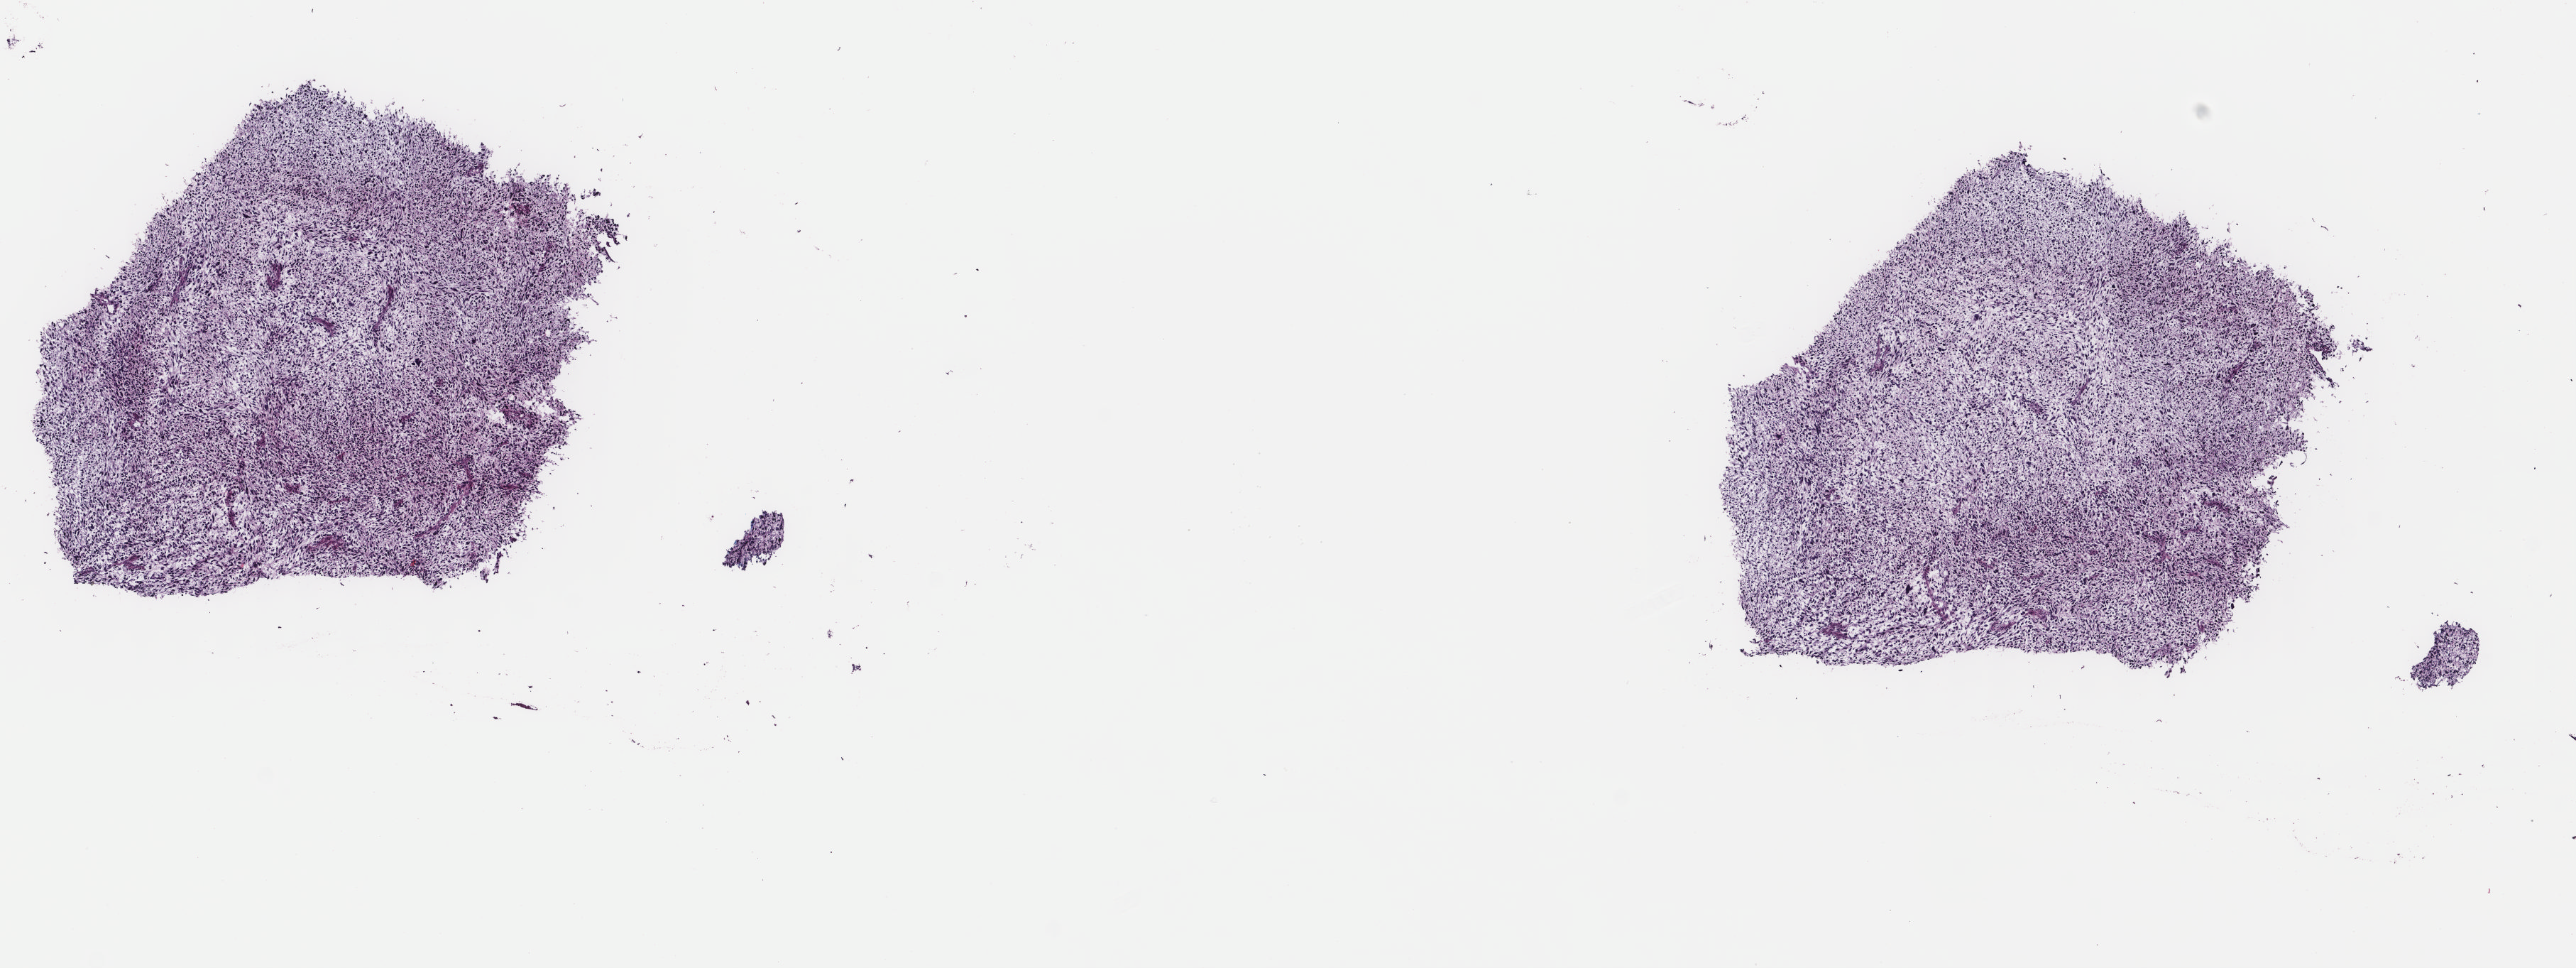
H&E-stained whole-slide image — shown as a low-resolution overview of the whole scanned area (about 14.4 x 5.4 mm, acquisition: 40x scan), frozen section, sample: primary tumour, retroperitoneum and peritoneum. Female, age 61 years at initial diagnosis. Pathologist review of this section (percent, as recorded): tumour cells 90%, tumour nuclei 90%, normal cells 0%, stromal cells 10%, necrosis 0%. Inflammatory infiltration, as recorded: lymphocyte infiltration 0%, monocyte infiltration 0%, neutrophil infiltration 0%.
Histologic diagnosis: Dedifferentiated liposarcoma.